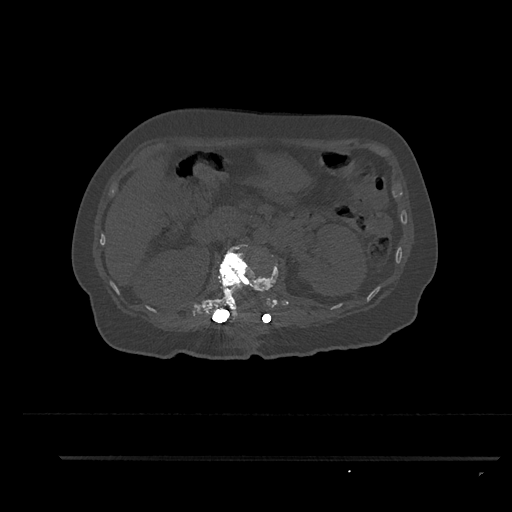
CT including the spine, one axial slice. Reconstruction kernel Br40s/3. 120 kVp. Bone window (W 1800 / L 400 HU). 512 × 512 image matrix, field of view 408 × 408 mm. Female patient, age 44 years. Case-level facts recorded for this patient, not image findings: primary cancer: renal.
Structures marked on this image (semi-automatic segmentation, software-assisted and operator-edited):
- L1 vertebra: bounding box (x1, y1, x2, y2) in pixels: (203, 244, 278, 322)